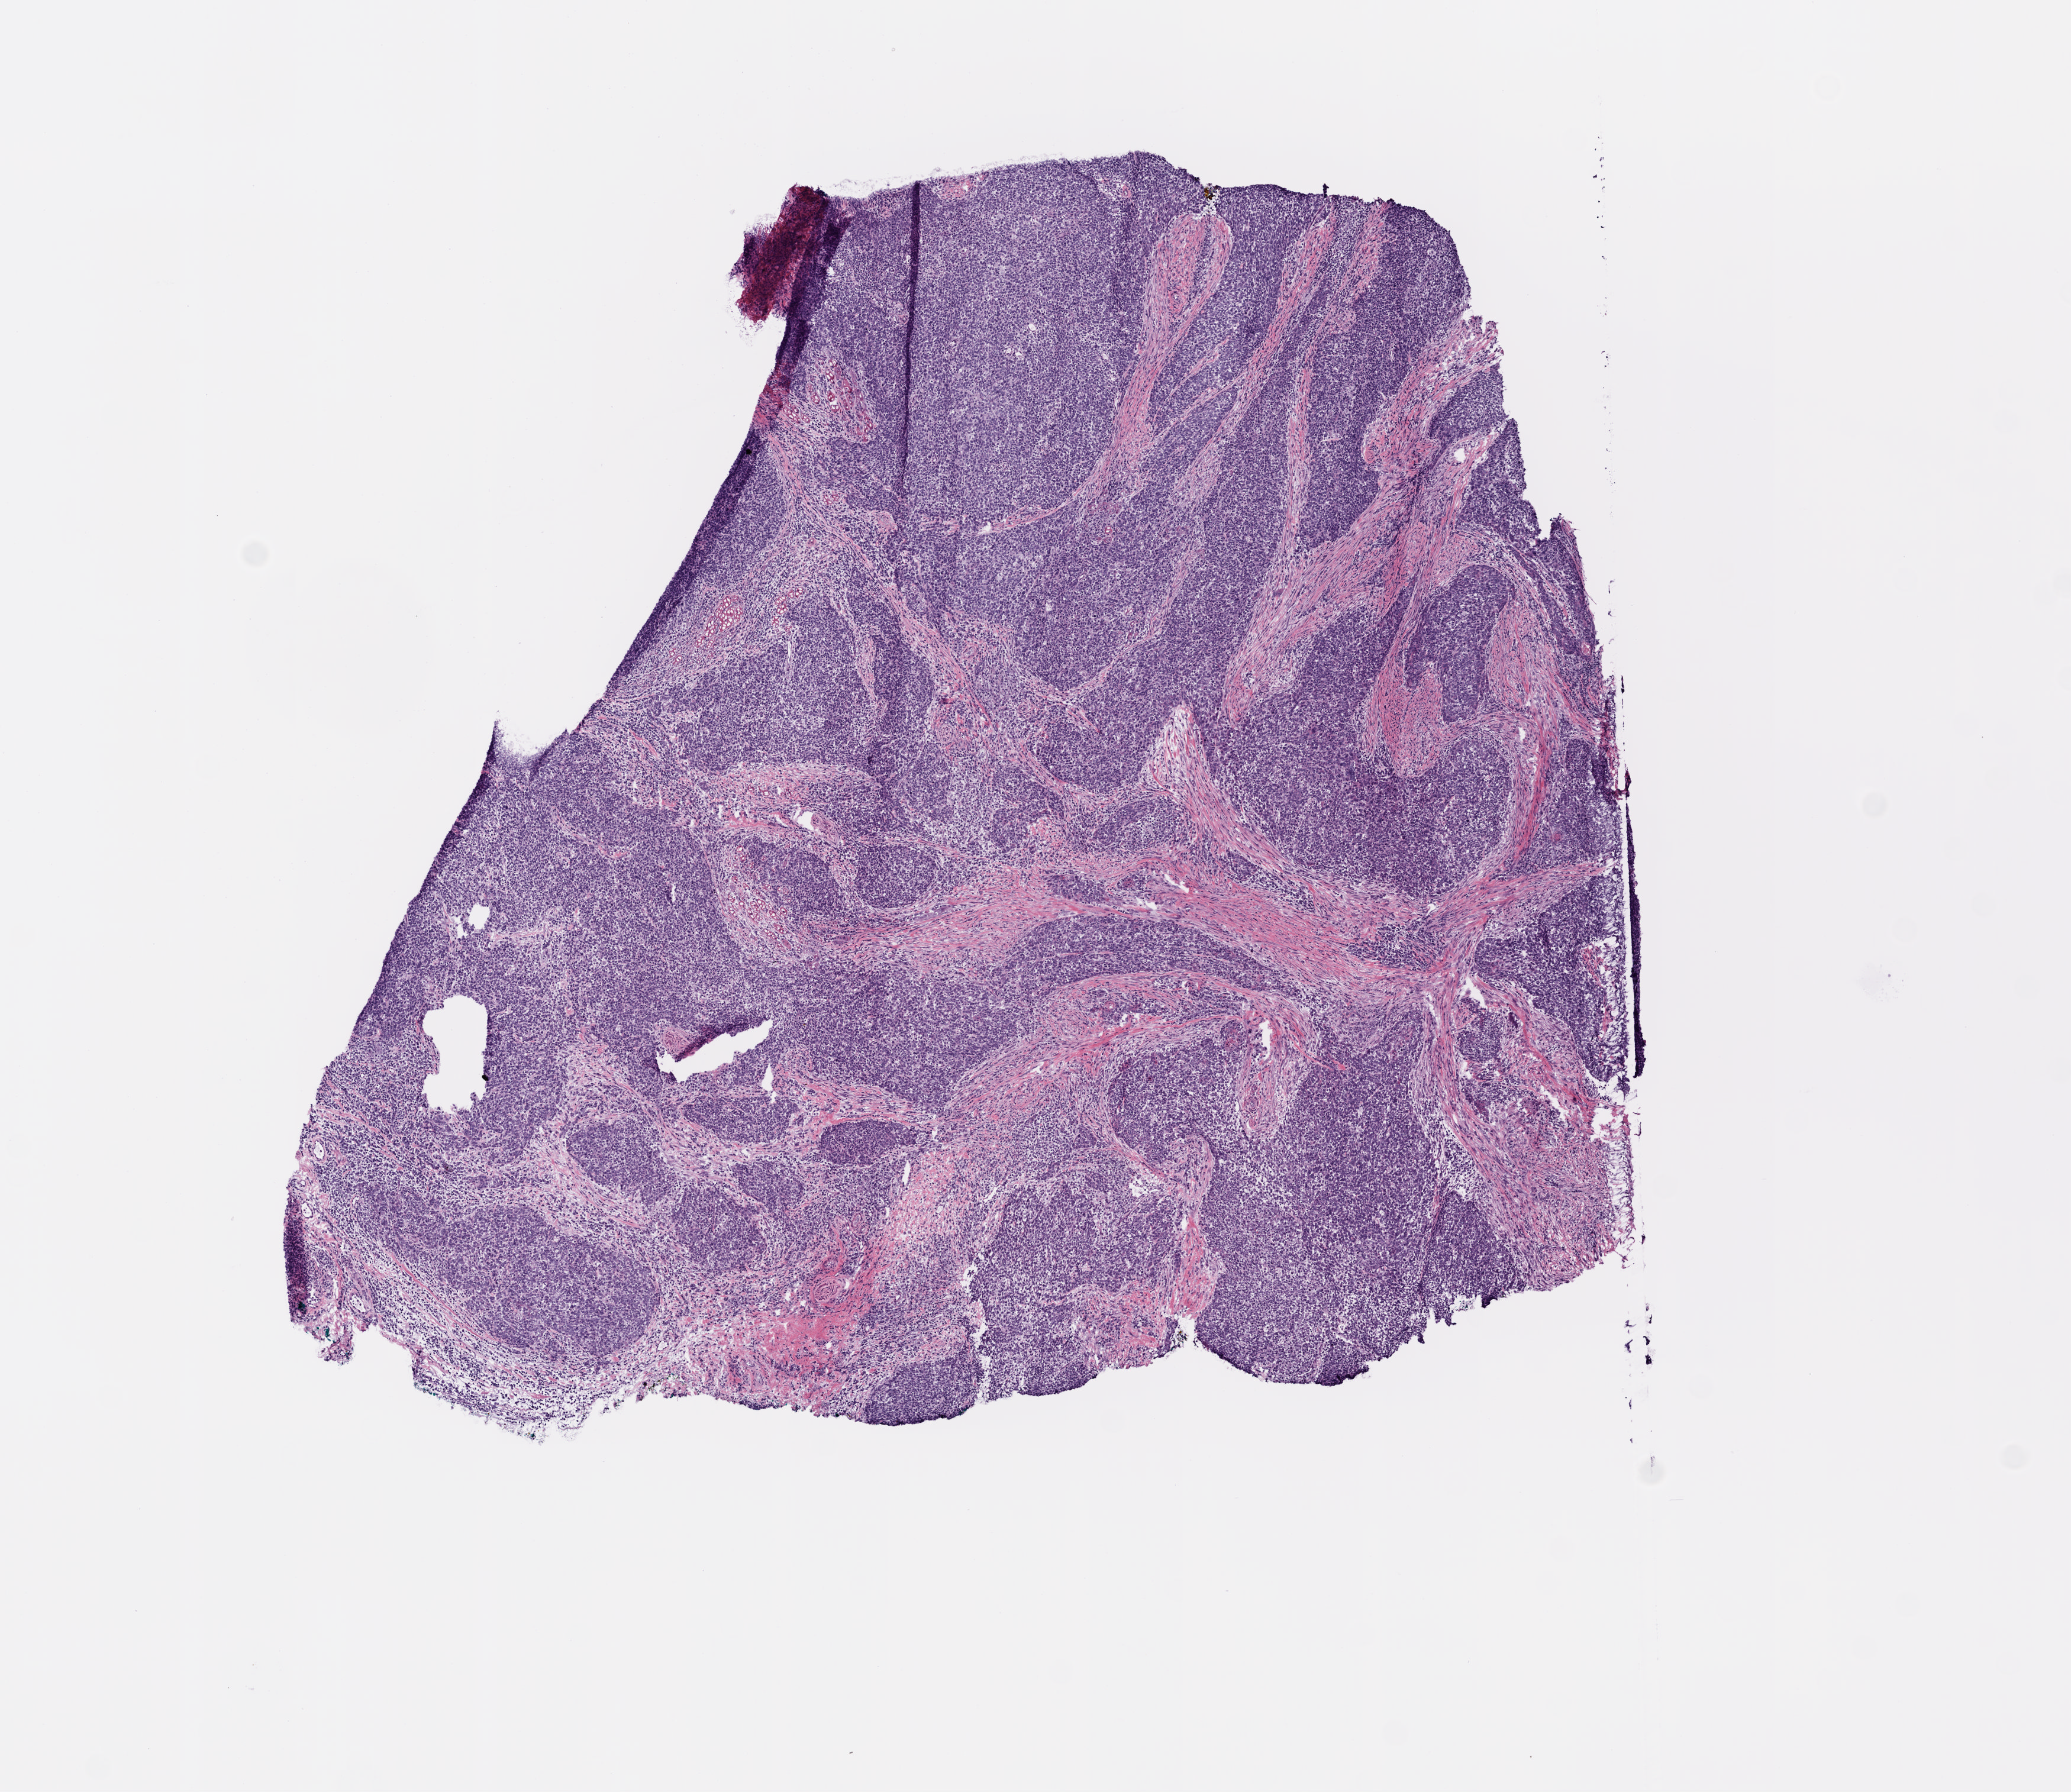
Whole-slide histology image, H&E, a low-resolution overview of the entire scanned area, about 7.0 x 6.1 mm, frozen section from the bottom of the tissue portion, sample: primary tumour, head and neck. Male, age 71 years at initial diagnosis. Histologic grade: G3 (poorly differentiated). Slide review estimates, as recorded: tumour cells 85%, tumour nuclei 70%, normal cells 0%, stromal cells 15%, necrosis 0%.
Lymph nodes positive (case pathology): 4 of 25 examined. Laterality: left. Pathologic diagnosis: Squamous cell carcinoma, NOS.